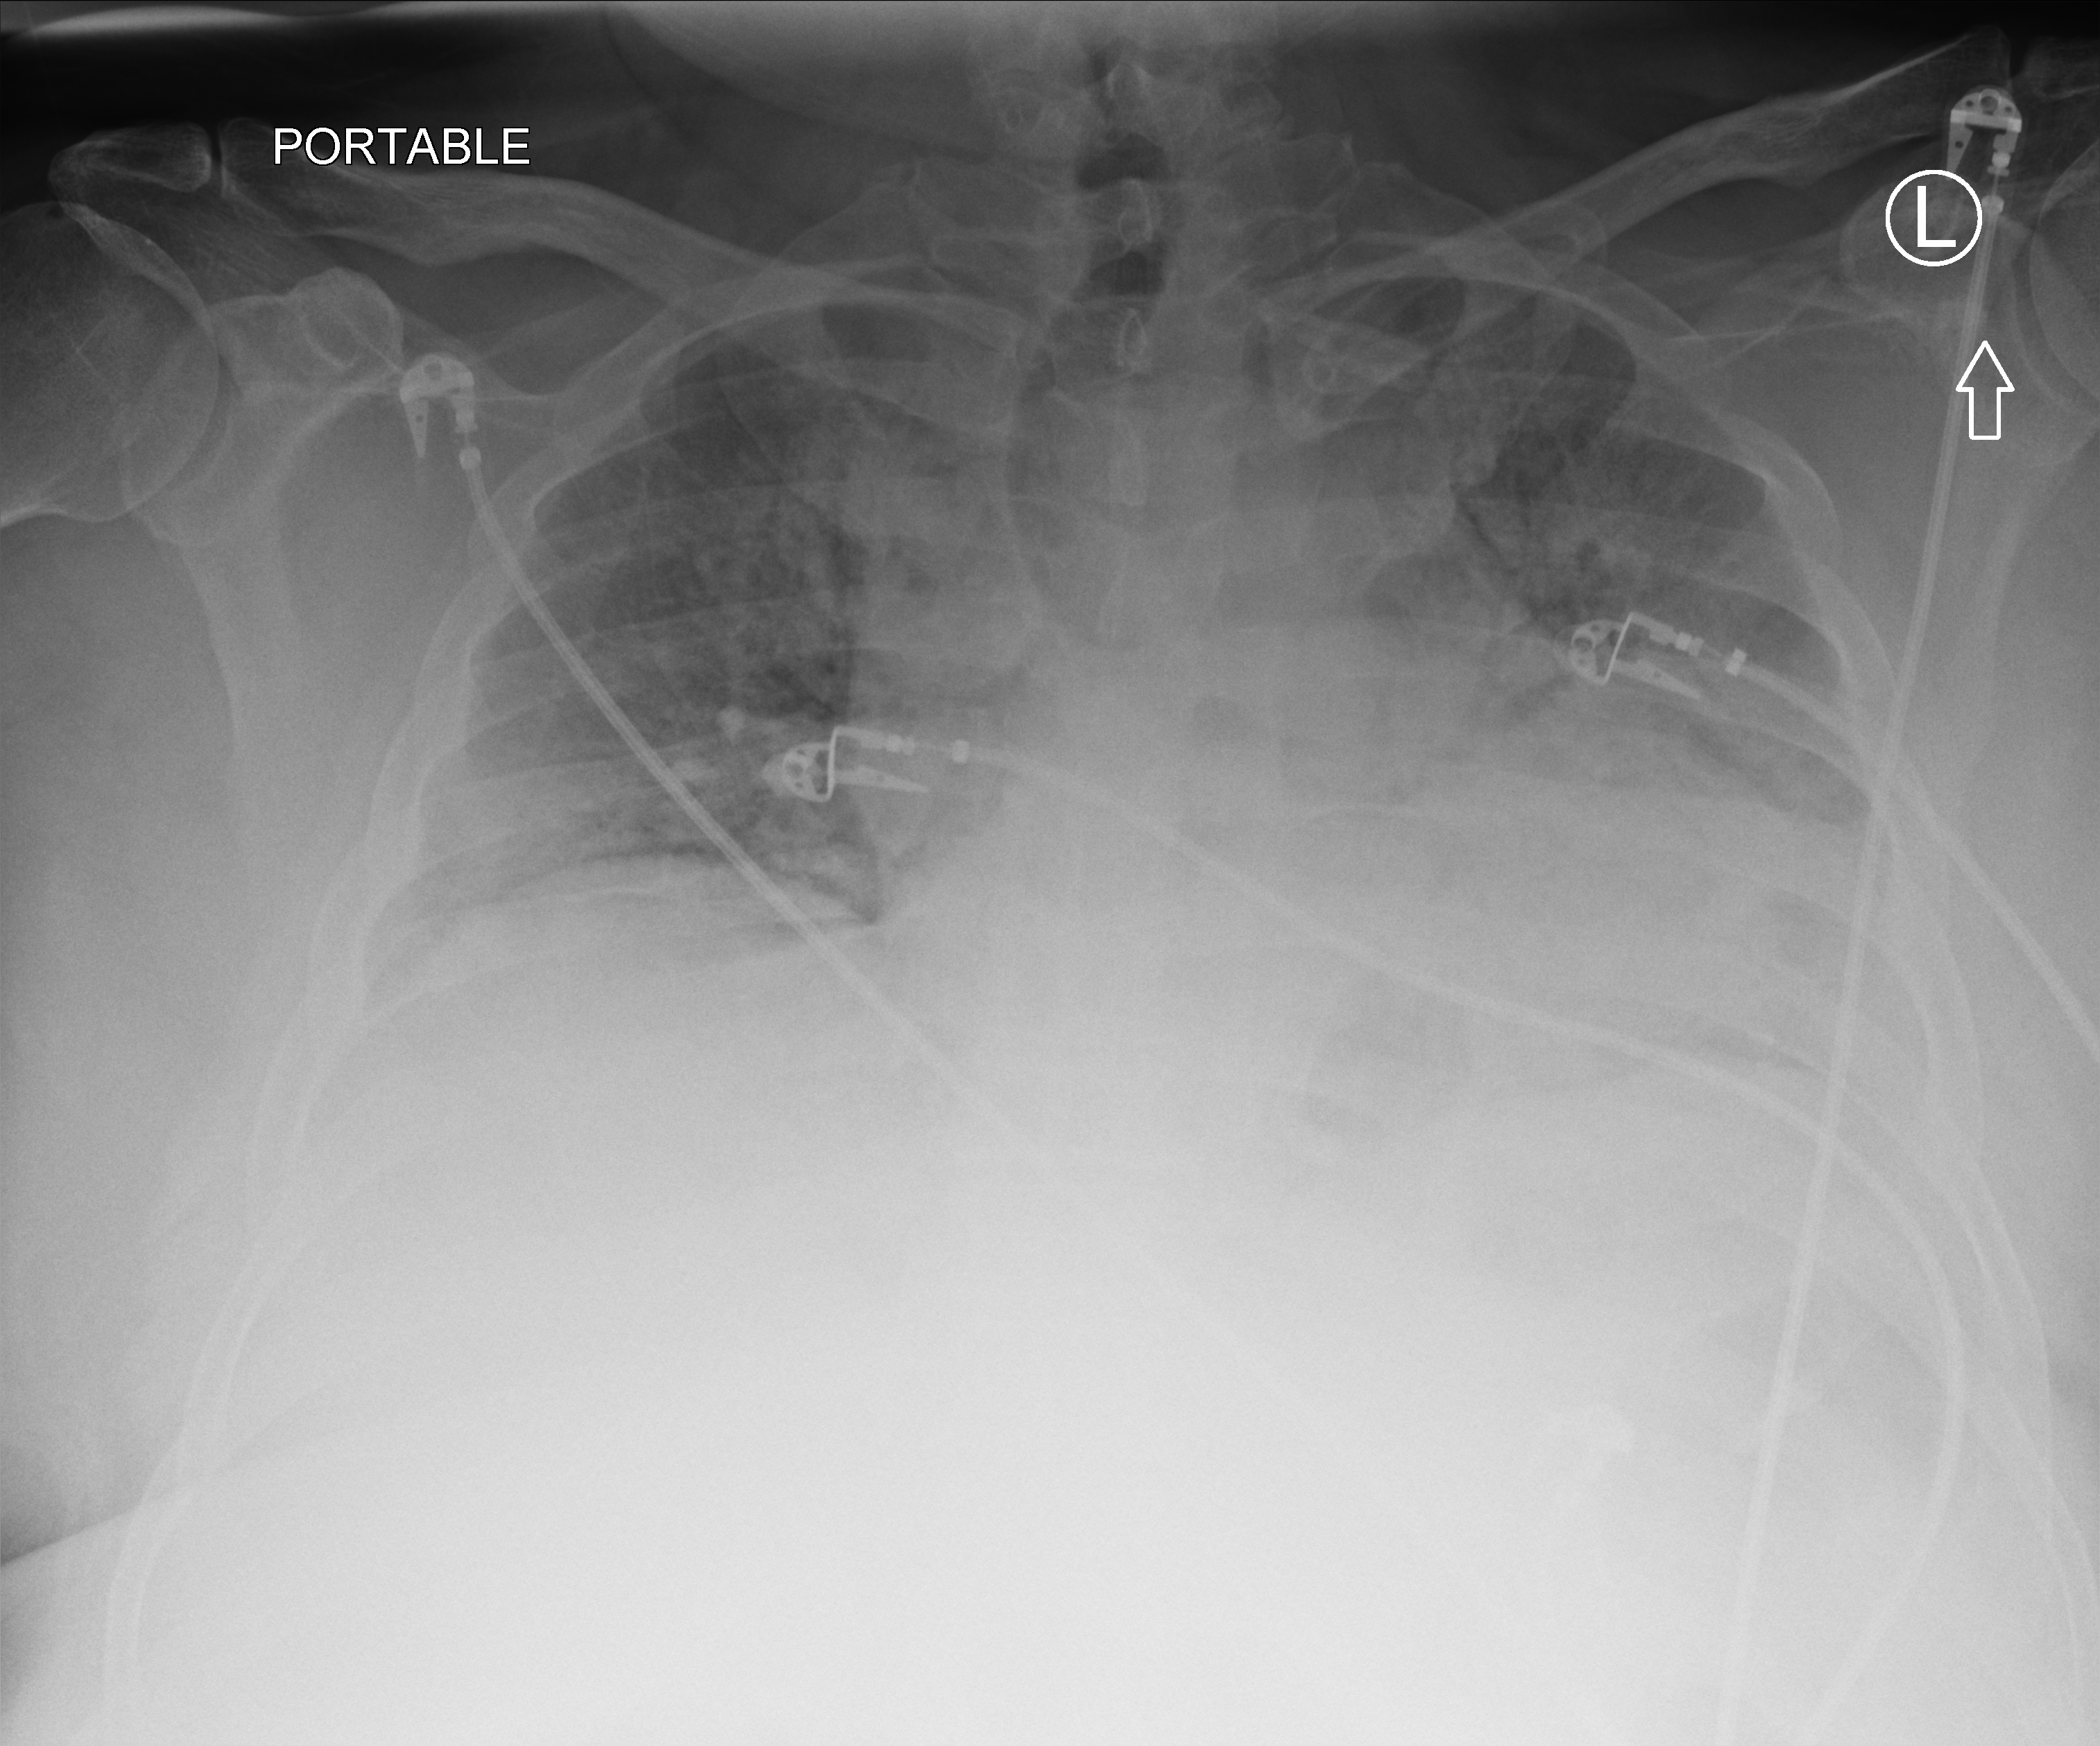
Chest X-ray (portable), anteroposterior (AP) projection. Adult patient hospitalised with COVID-19, age 18–59 years.
Hospital-stay facts (about this admission, not read from this image; timing relative to this image not recorded): admitted to intensive care during this hospital stay: yes; hypertension (admission record): yes; length of hospital stay: 26 days.